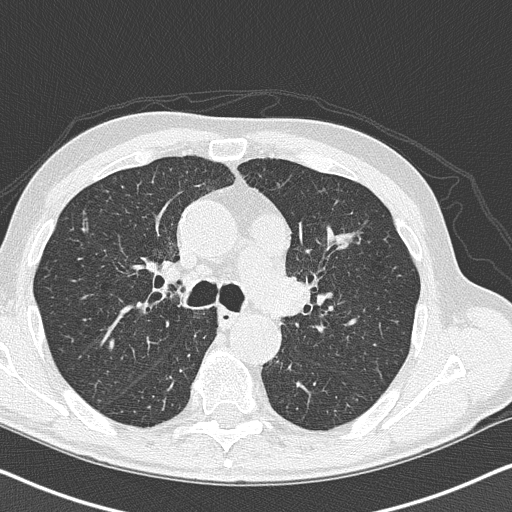
Low-dose screening chest CT, one axial slice. Reconstruction kernel B50f. Lung window (W 1500 / L -600 HU). 2 mm slice thickness. 512 × 512 image matrix, field of view 330 × 330 mm.
Annotated regions visible in this slice (manually delineated by an expert):
- lesion 1 (tumor, upper lobe of left lung): box from (x=335, y=233) to (x=355, y=246) px